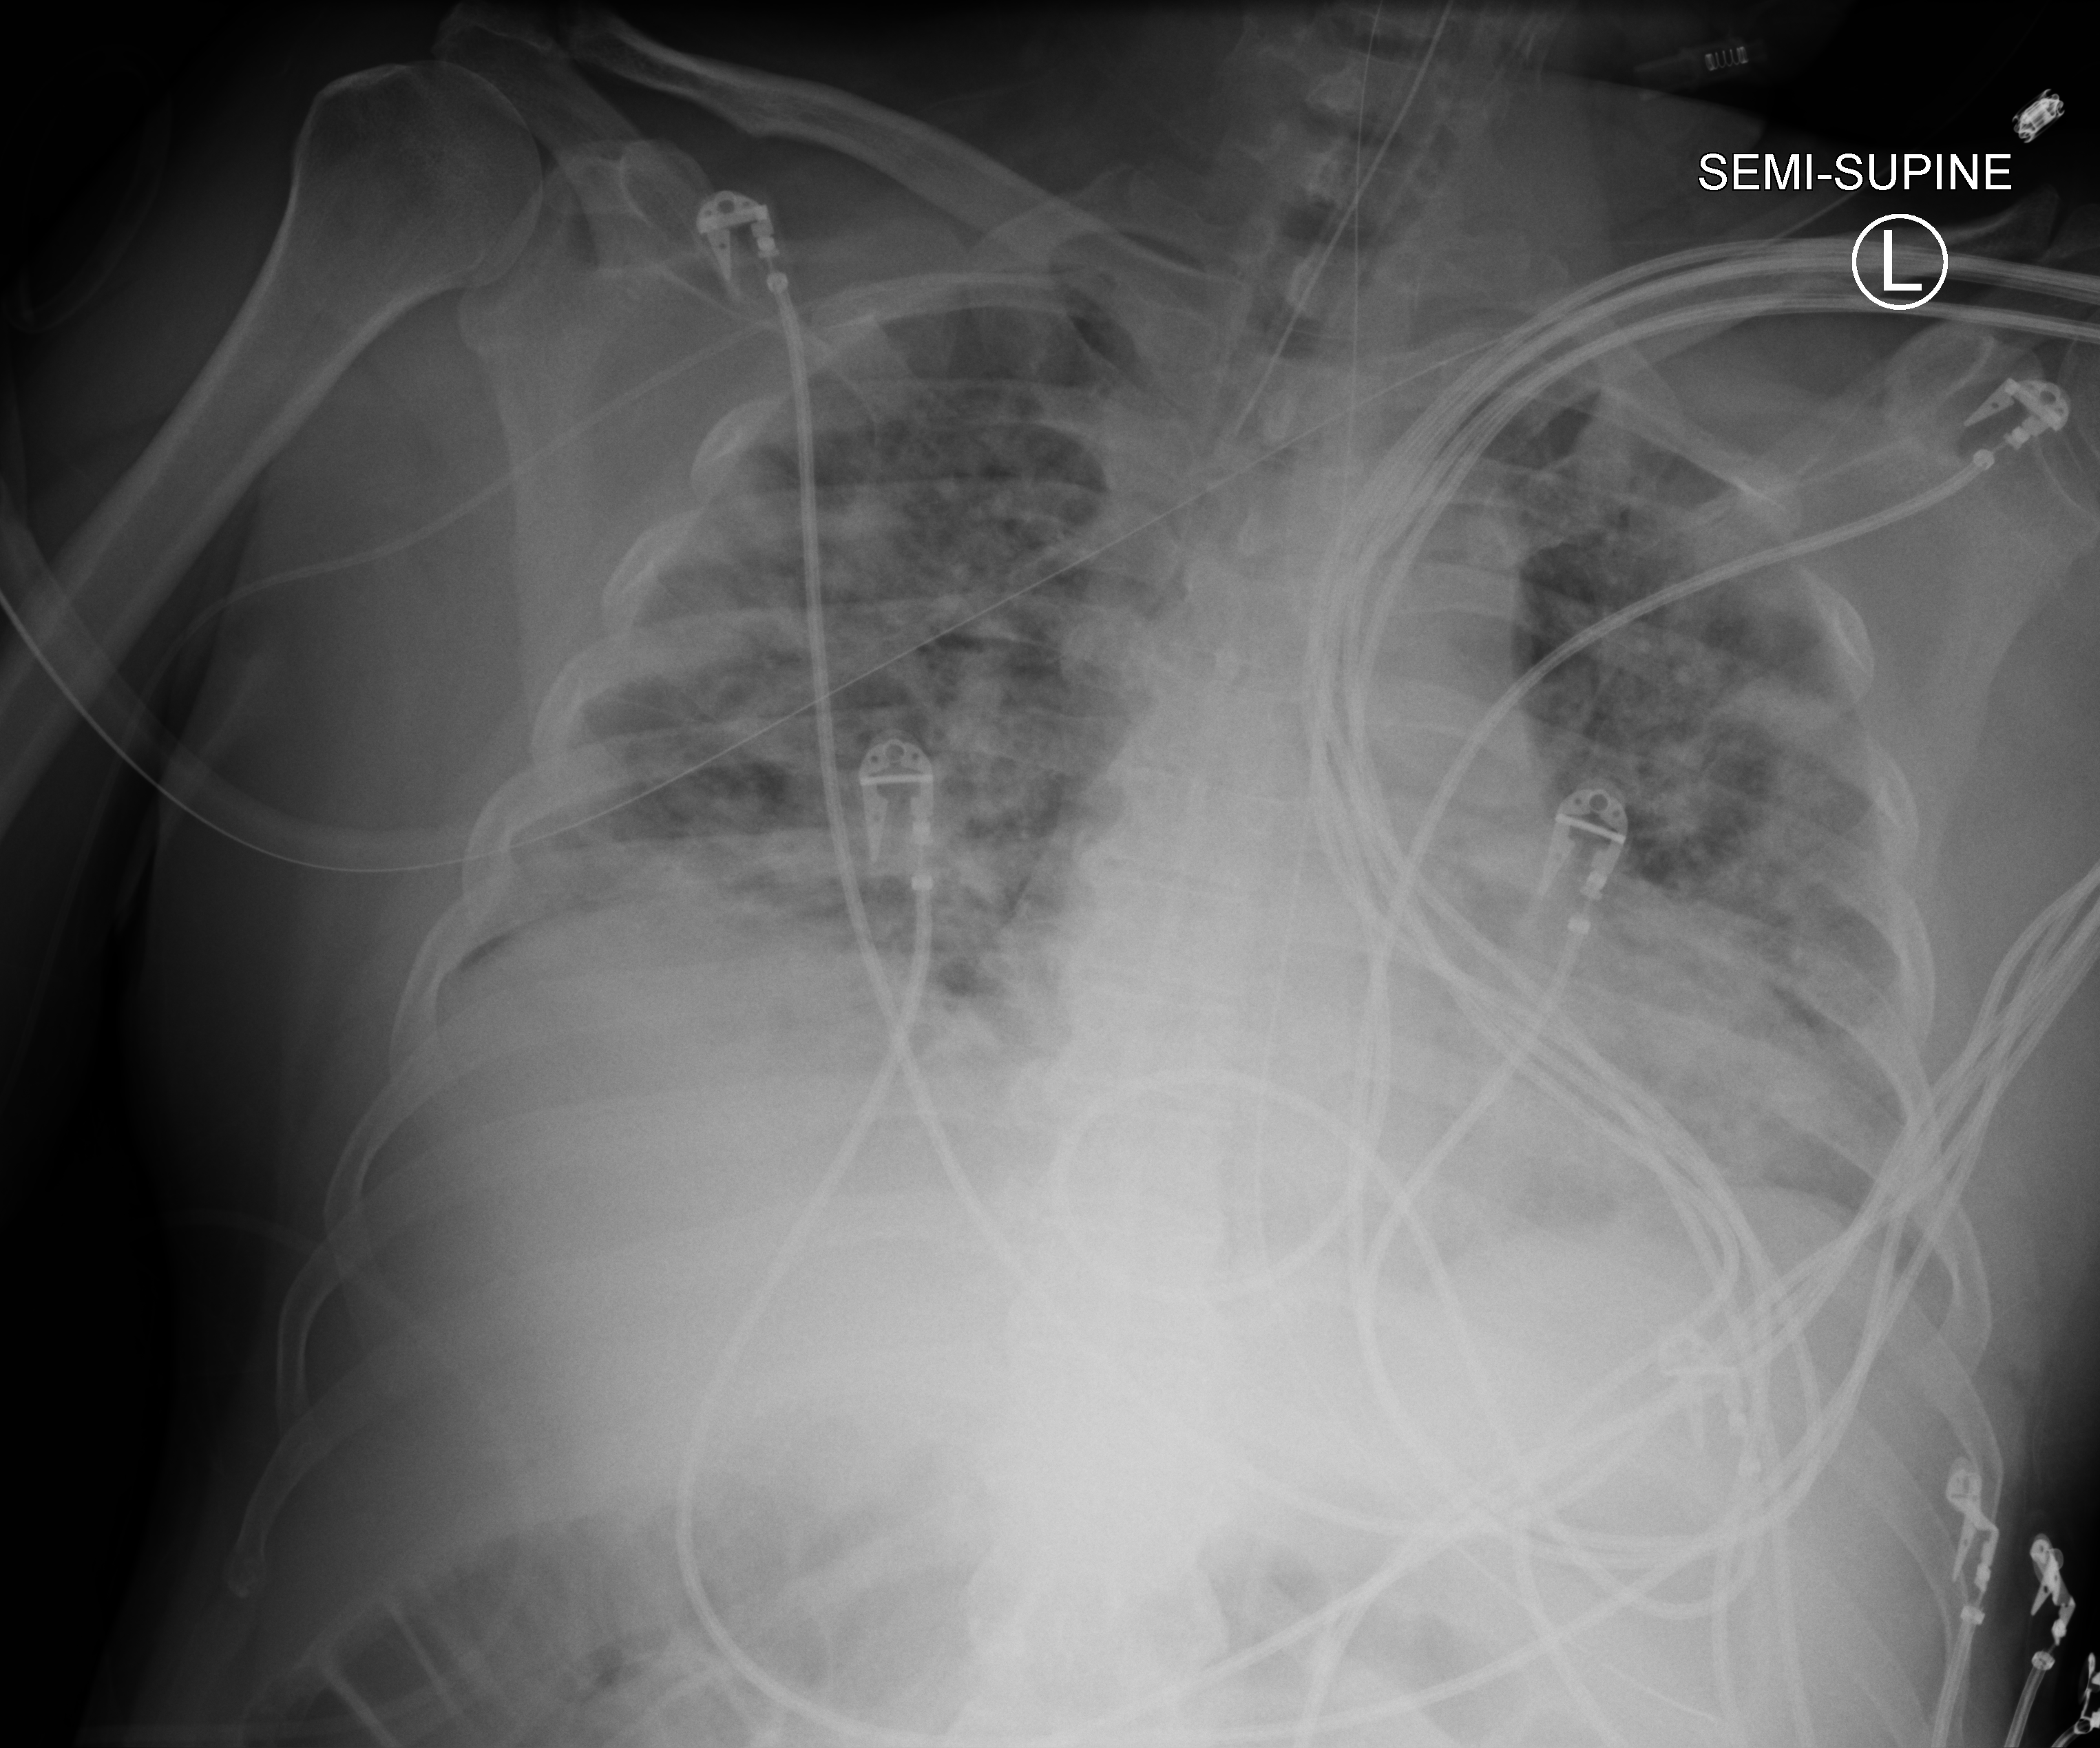
Portable chest radiograph, anteroposterior (AP) projection. Patient hospitalised with COVID-19; male, aged 18–59 years.
Admission-level facts for this patient (not findings on this image; timing relative to this image not recorded): diabetes (admission record): yes; hypertension (admission record): yes; mechanically ventilated during this hospital stay: yes.